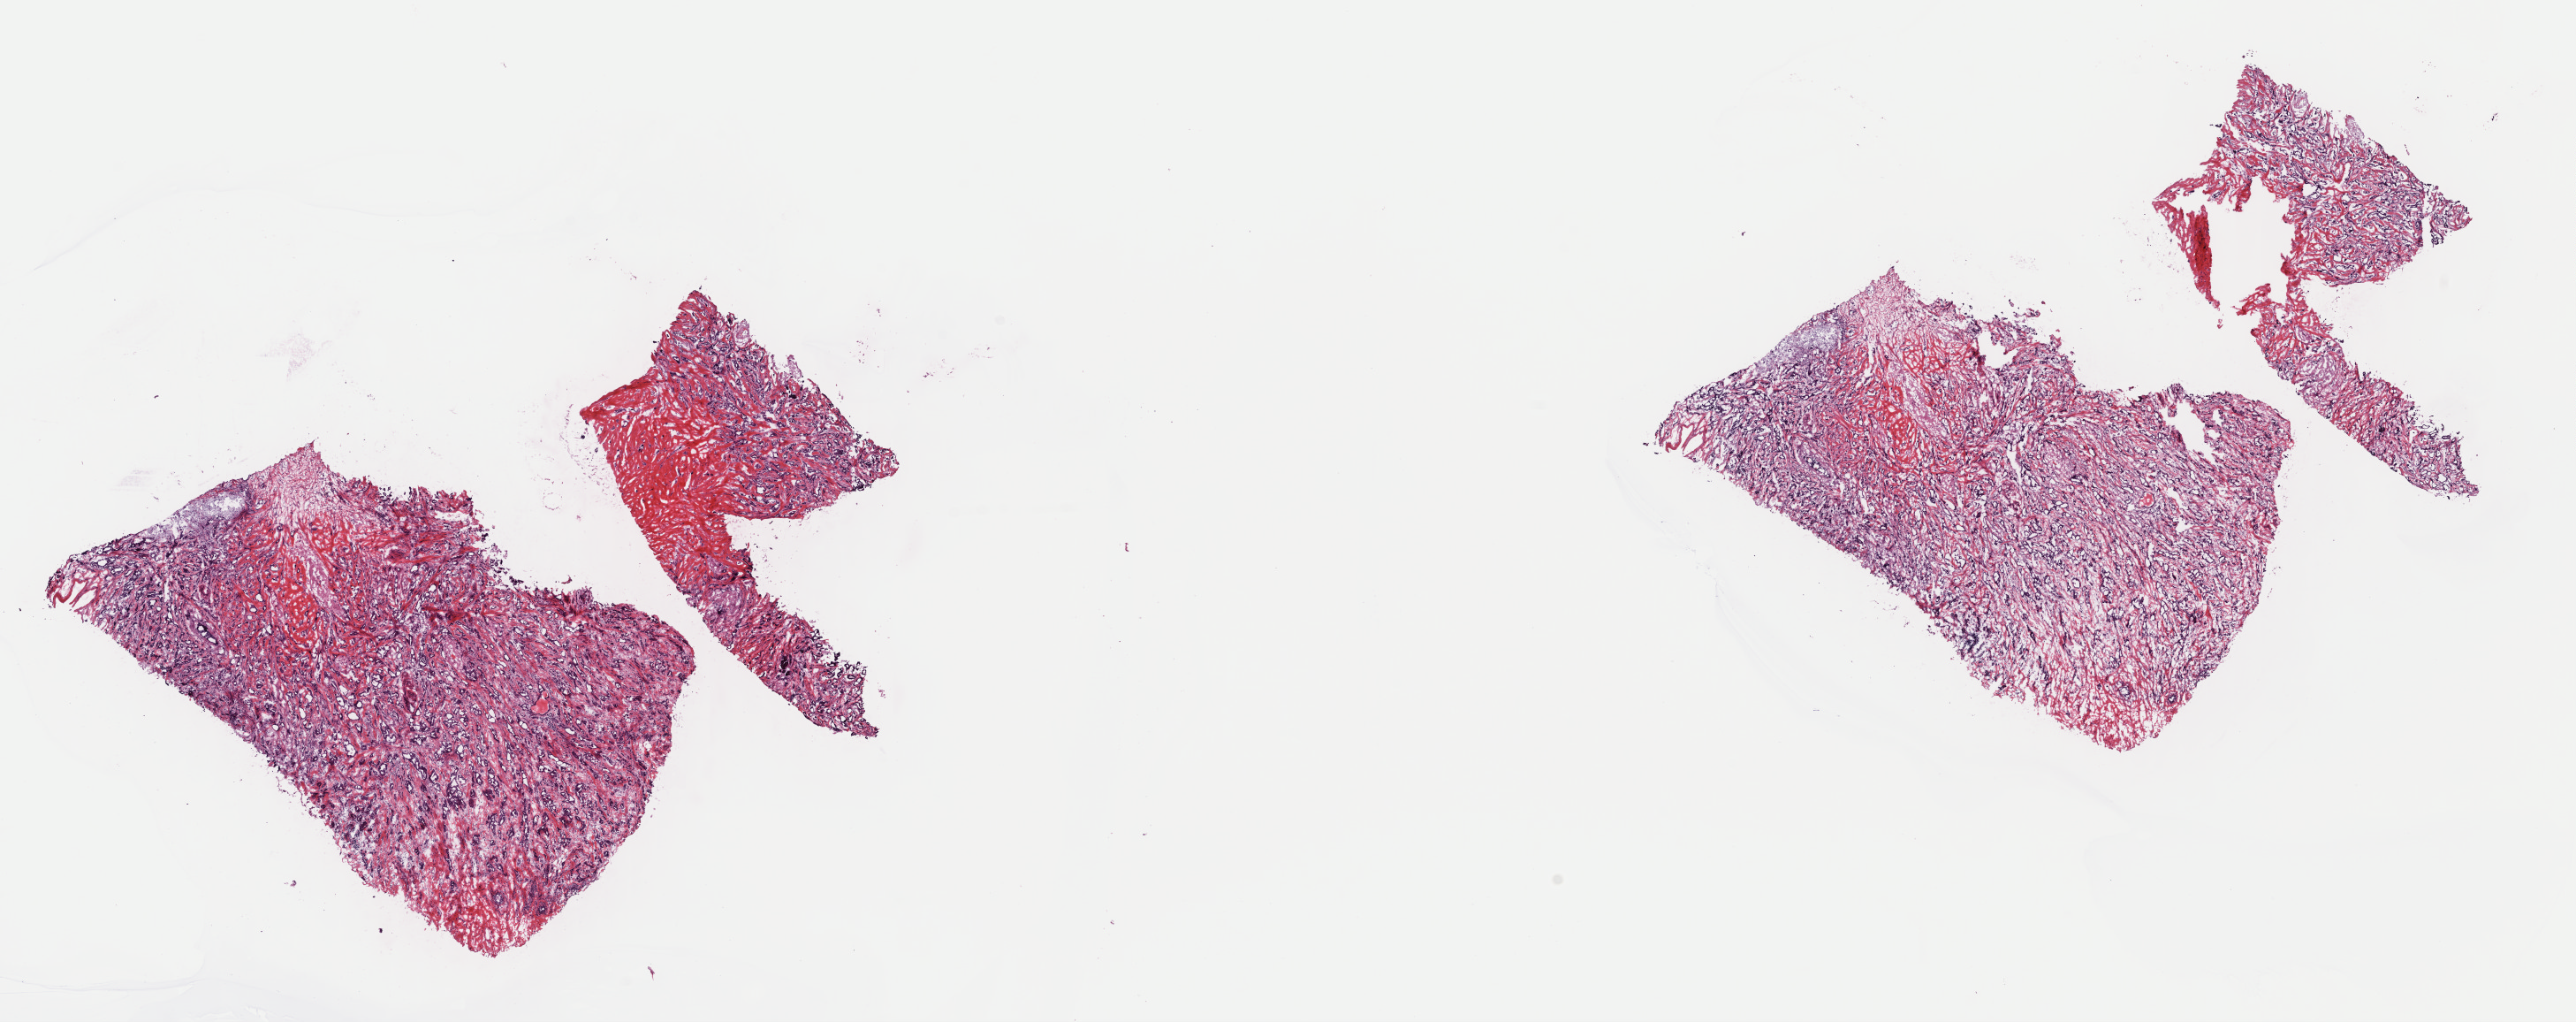
Hematoxylin and eosin (H&E) stained whole-slide image, a low-resolution overview of the entire scanned area, about 23.0 x 9.1 mm (acquisition: 40x scan). Frozen section from the top of the tissue portion. Breast, primary tumour sample. Patient: female, age at initial diagnosis 53 years. Pathologist review of this section (percent, as recorded): tumour cells 100%, tumour nuclei 75%, normal cells 0%, stromal cells 0%, necrosis 0%. Inflammatory infiltration, as recorded: lymphocyte infiltration 3%, monocyte infiltration 0%, neutrophil infiltration 0%.
AJCC pathologic stage: IIA. Diagnosis: Tubular adenocarcinoma.